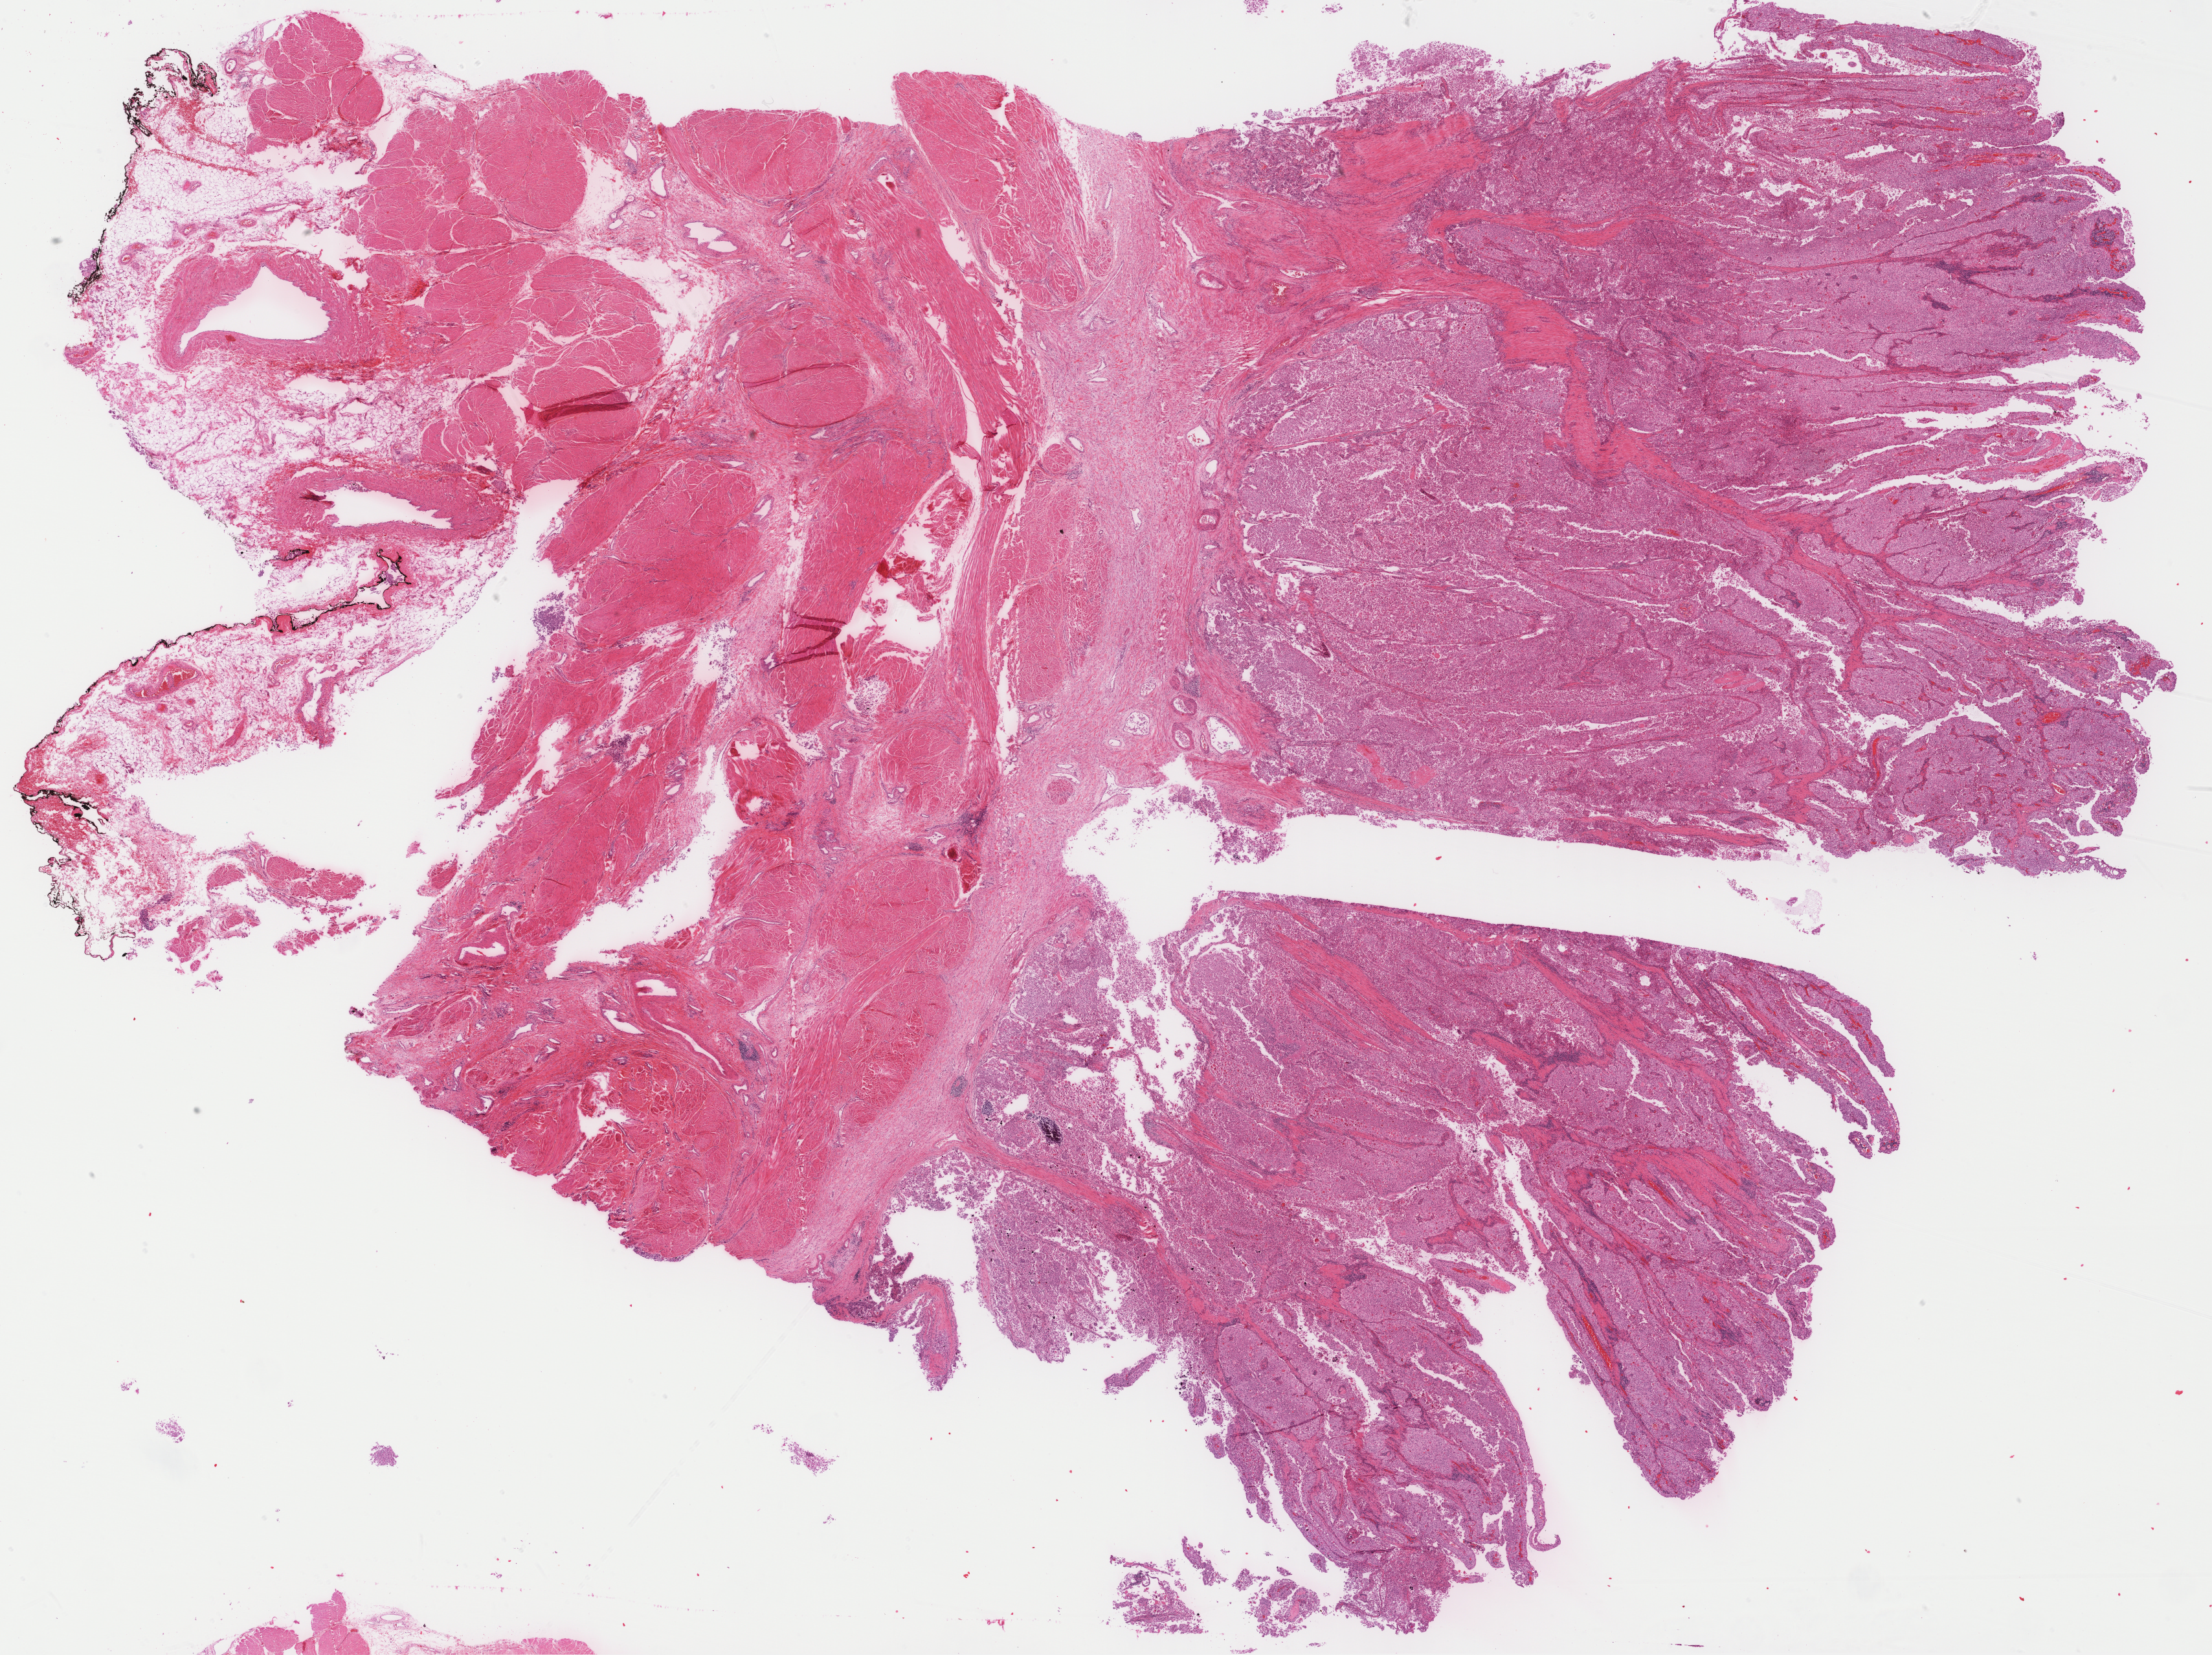
Digitized H&E-stained tissue section (whole slide) — low-resolution overview of the scanned area, about 27.7 x 20.7 mm (acquisition: 40x scan). Formalin-fixed paraffin-embedded (FFPE) diagnostic section. Primary tumour sample from the bladder. Male, age 53 years at initial diagnosis. Histologic grade: high grade.
AJCC pathologic stage: III. Histologic diagnosis: Papillary transitional cell carcinoma.